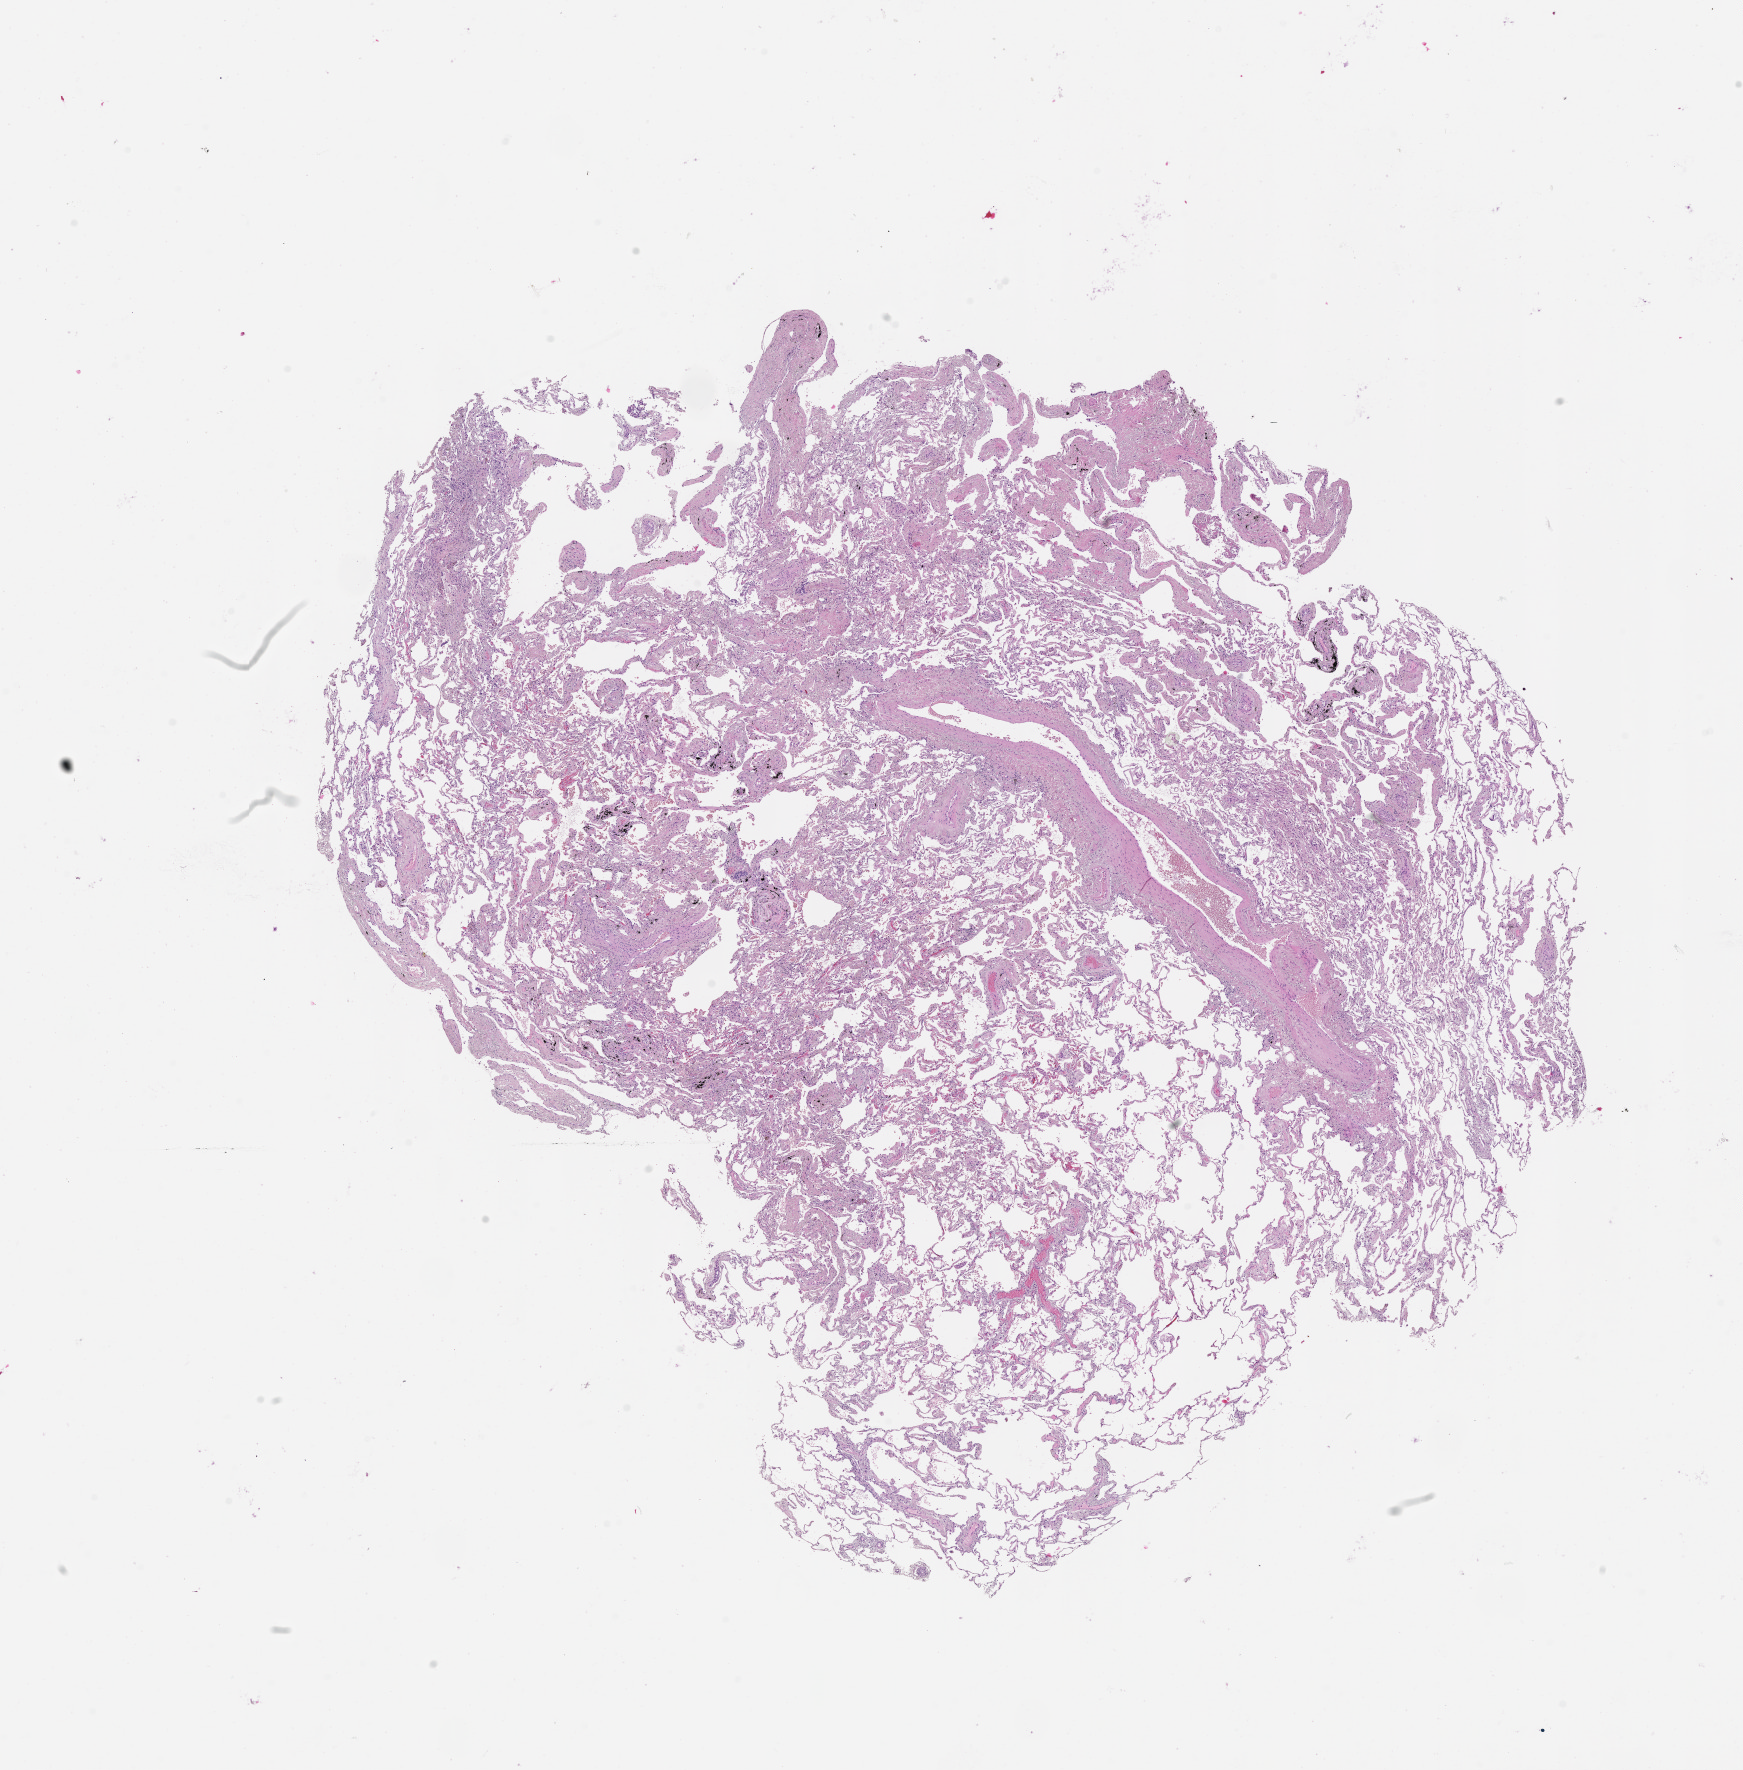
H&E-stained whole-slide image, whole scanned area (about 14.0 x 14.2 mm, from a 20x scan) shown as a low-resolution overview, lung, normal (non-tumour) tissue. Male, 77 y/o.
This section: normal (non-tumour) tissue from the same patient. Patient diagnosis (cohort enrolment): squamous cell carcinoma (lung).